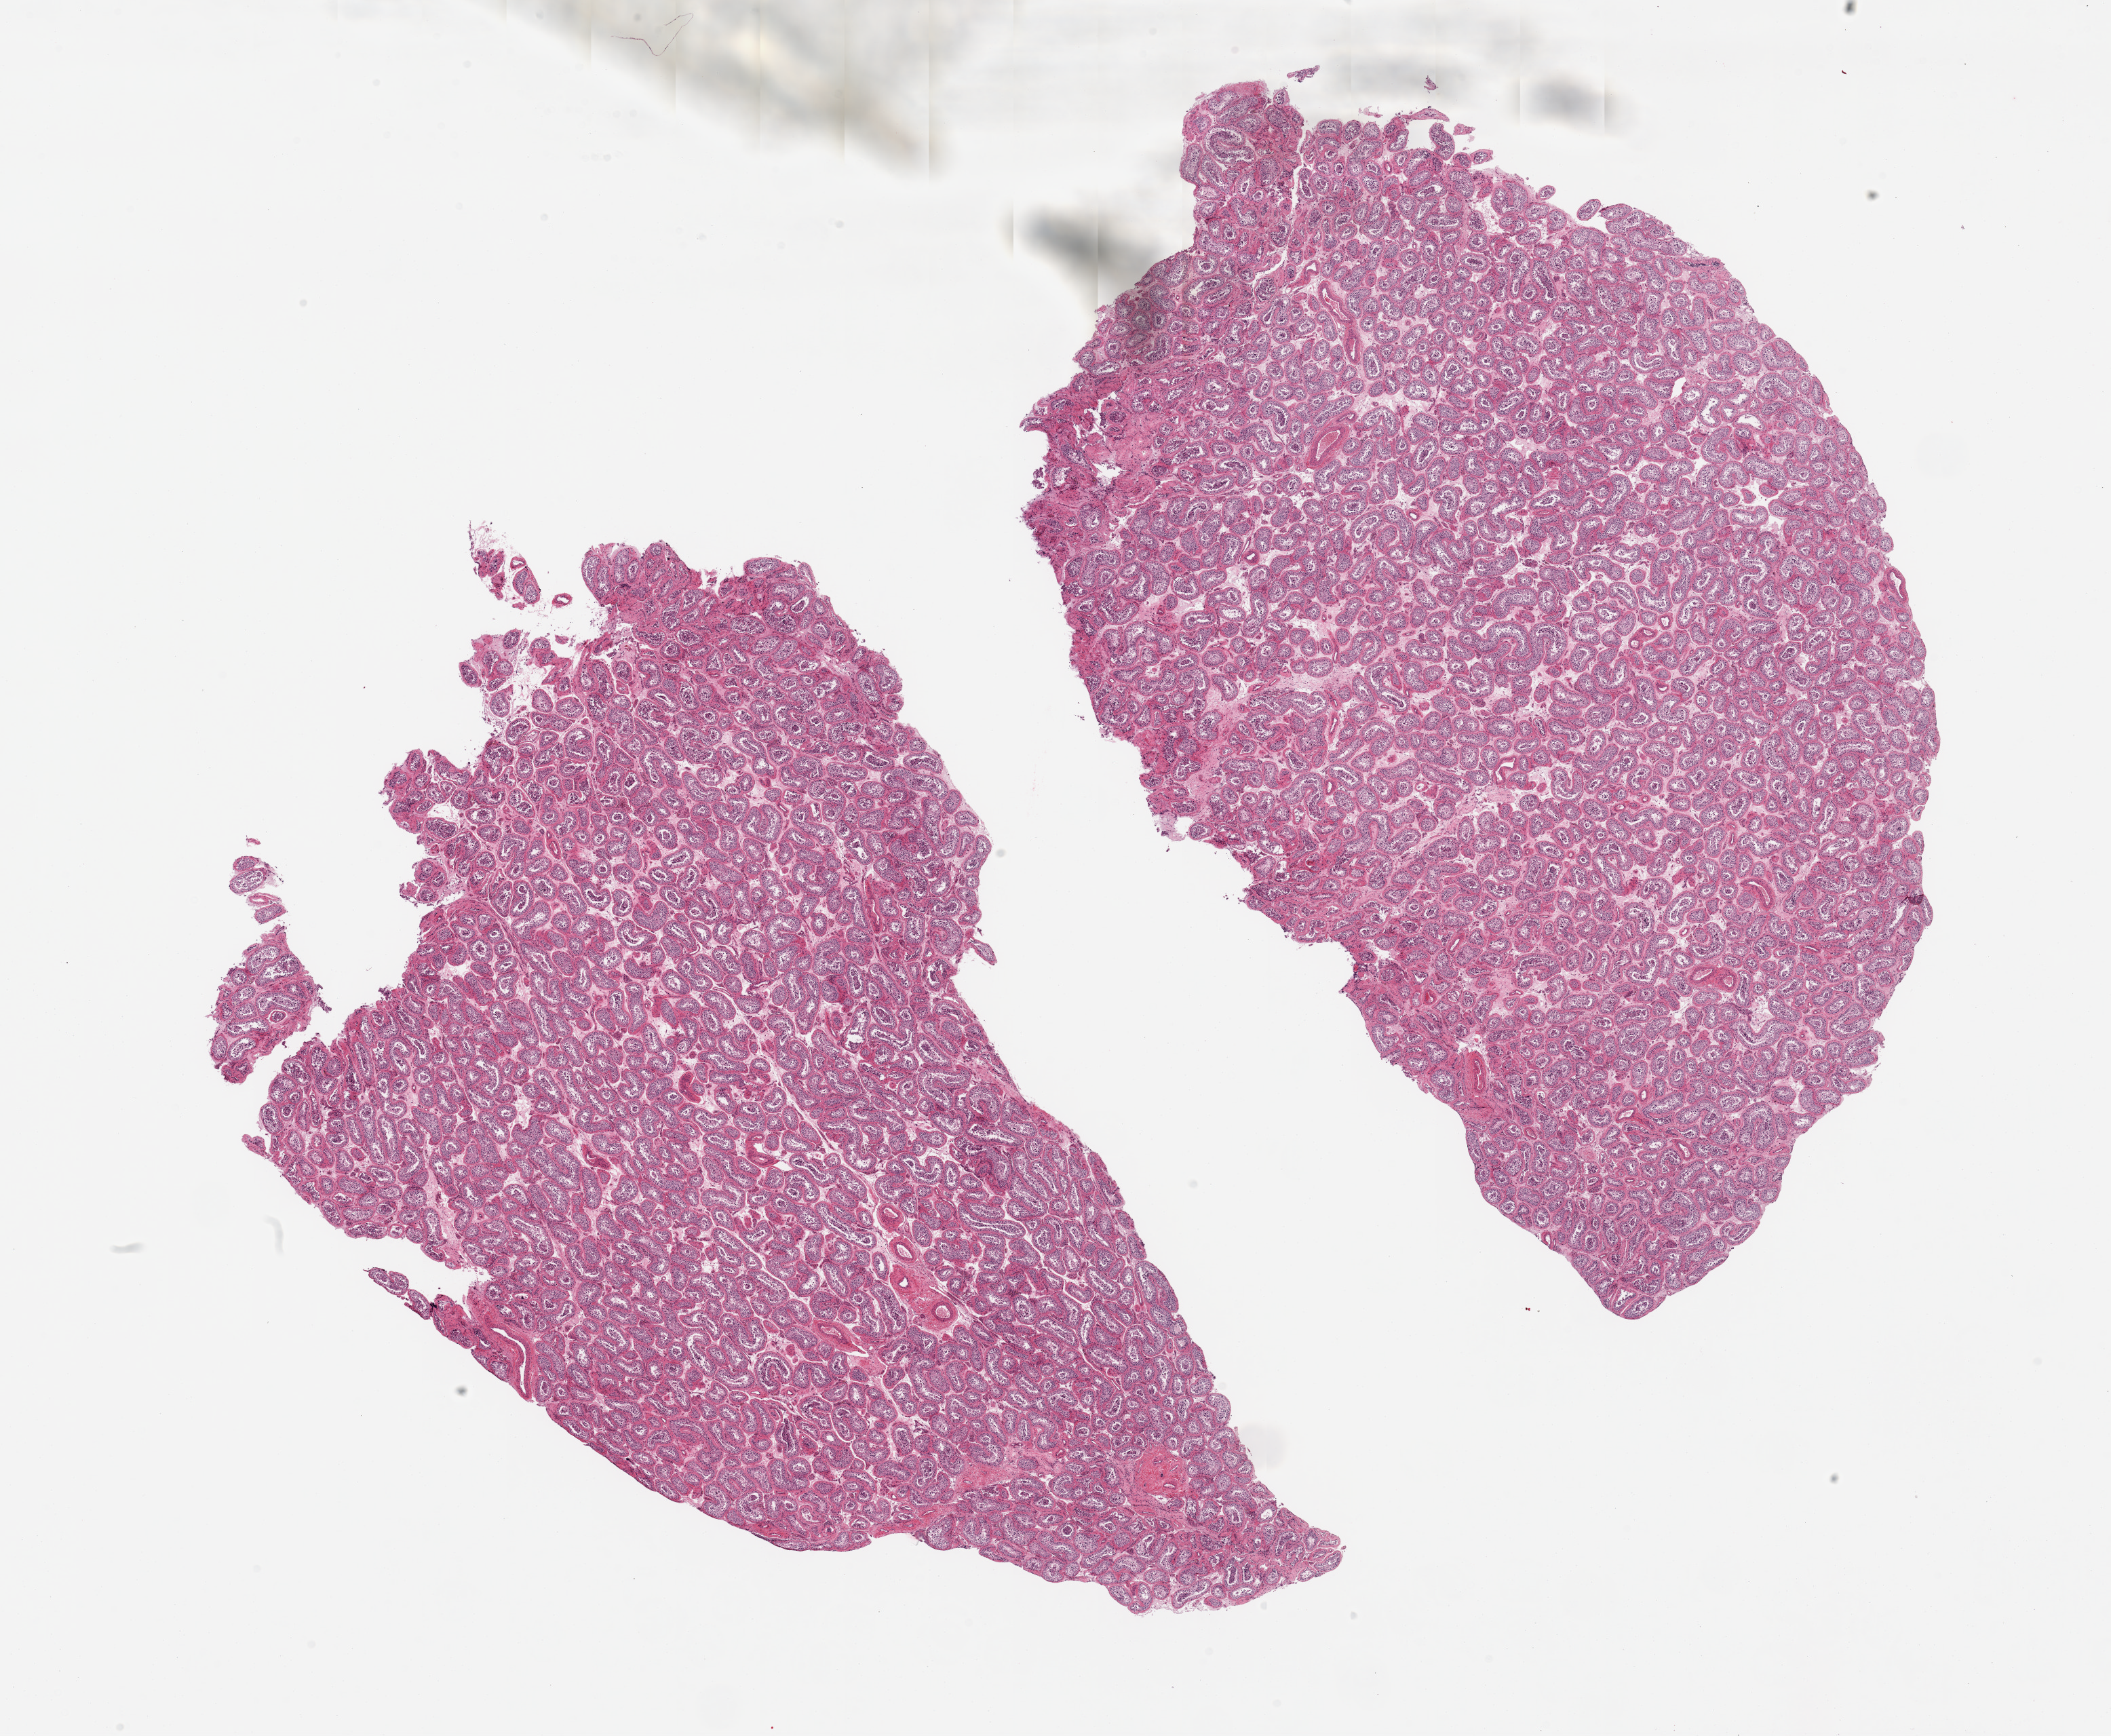
Digitized haematoxylin and eosin-stained section, brightfield, whole scanned area (about 24.6 x 20.2 mm) shown as a low-resolution overview; PAXgene-fixed paraffin-embedded (PFPE) section; target tissue: testis; donor tissue sample. Donor: male.
Pathologist's review note for this sample: 2 pieces; spermatogenesis present.